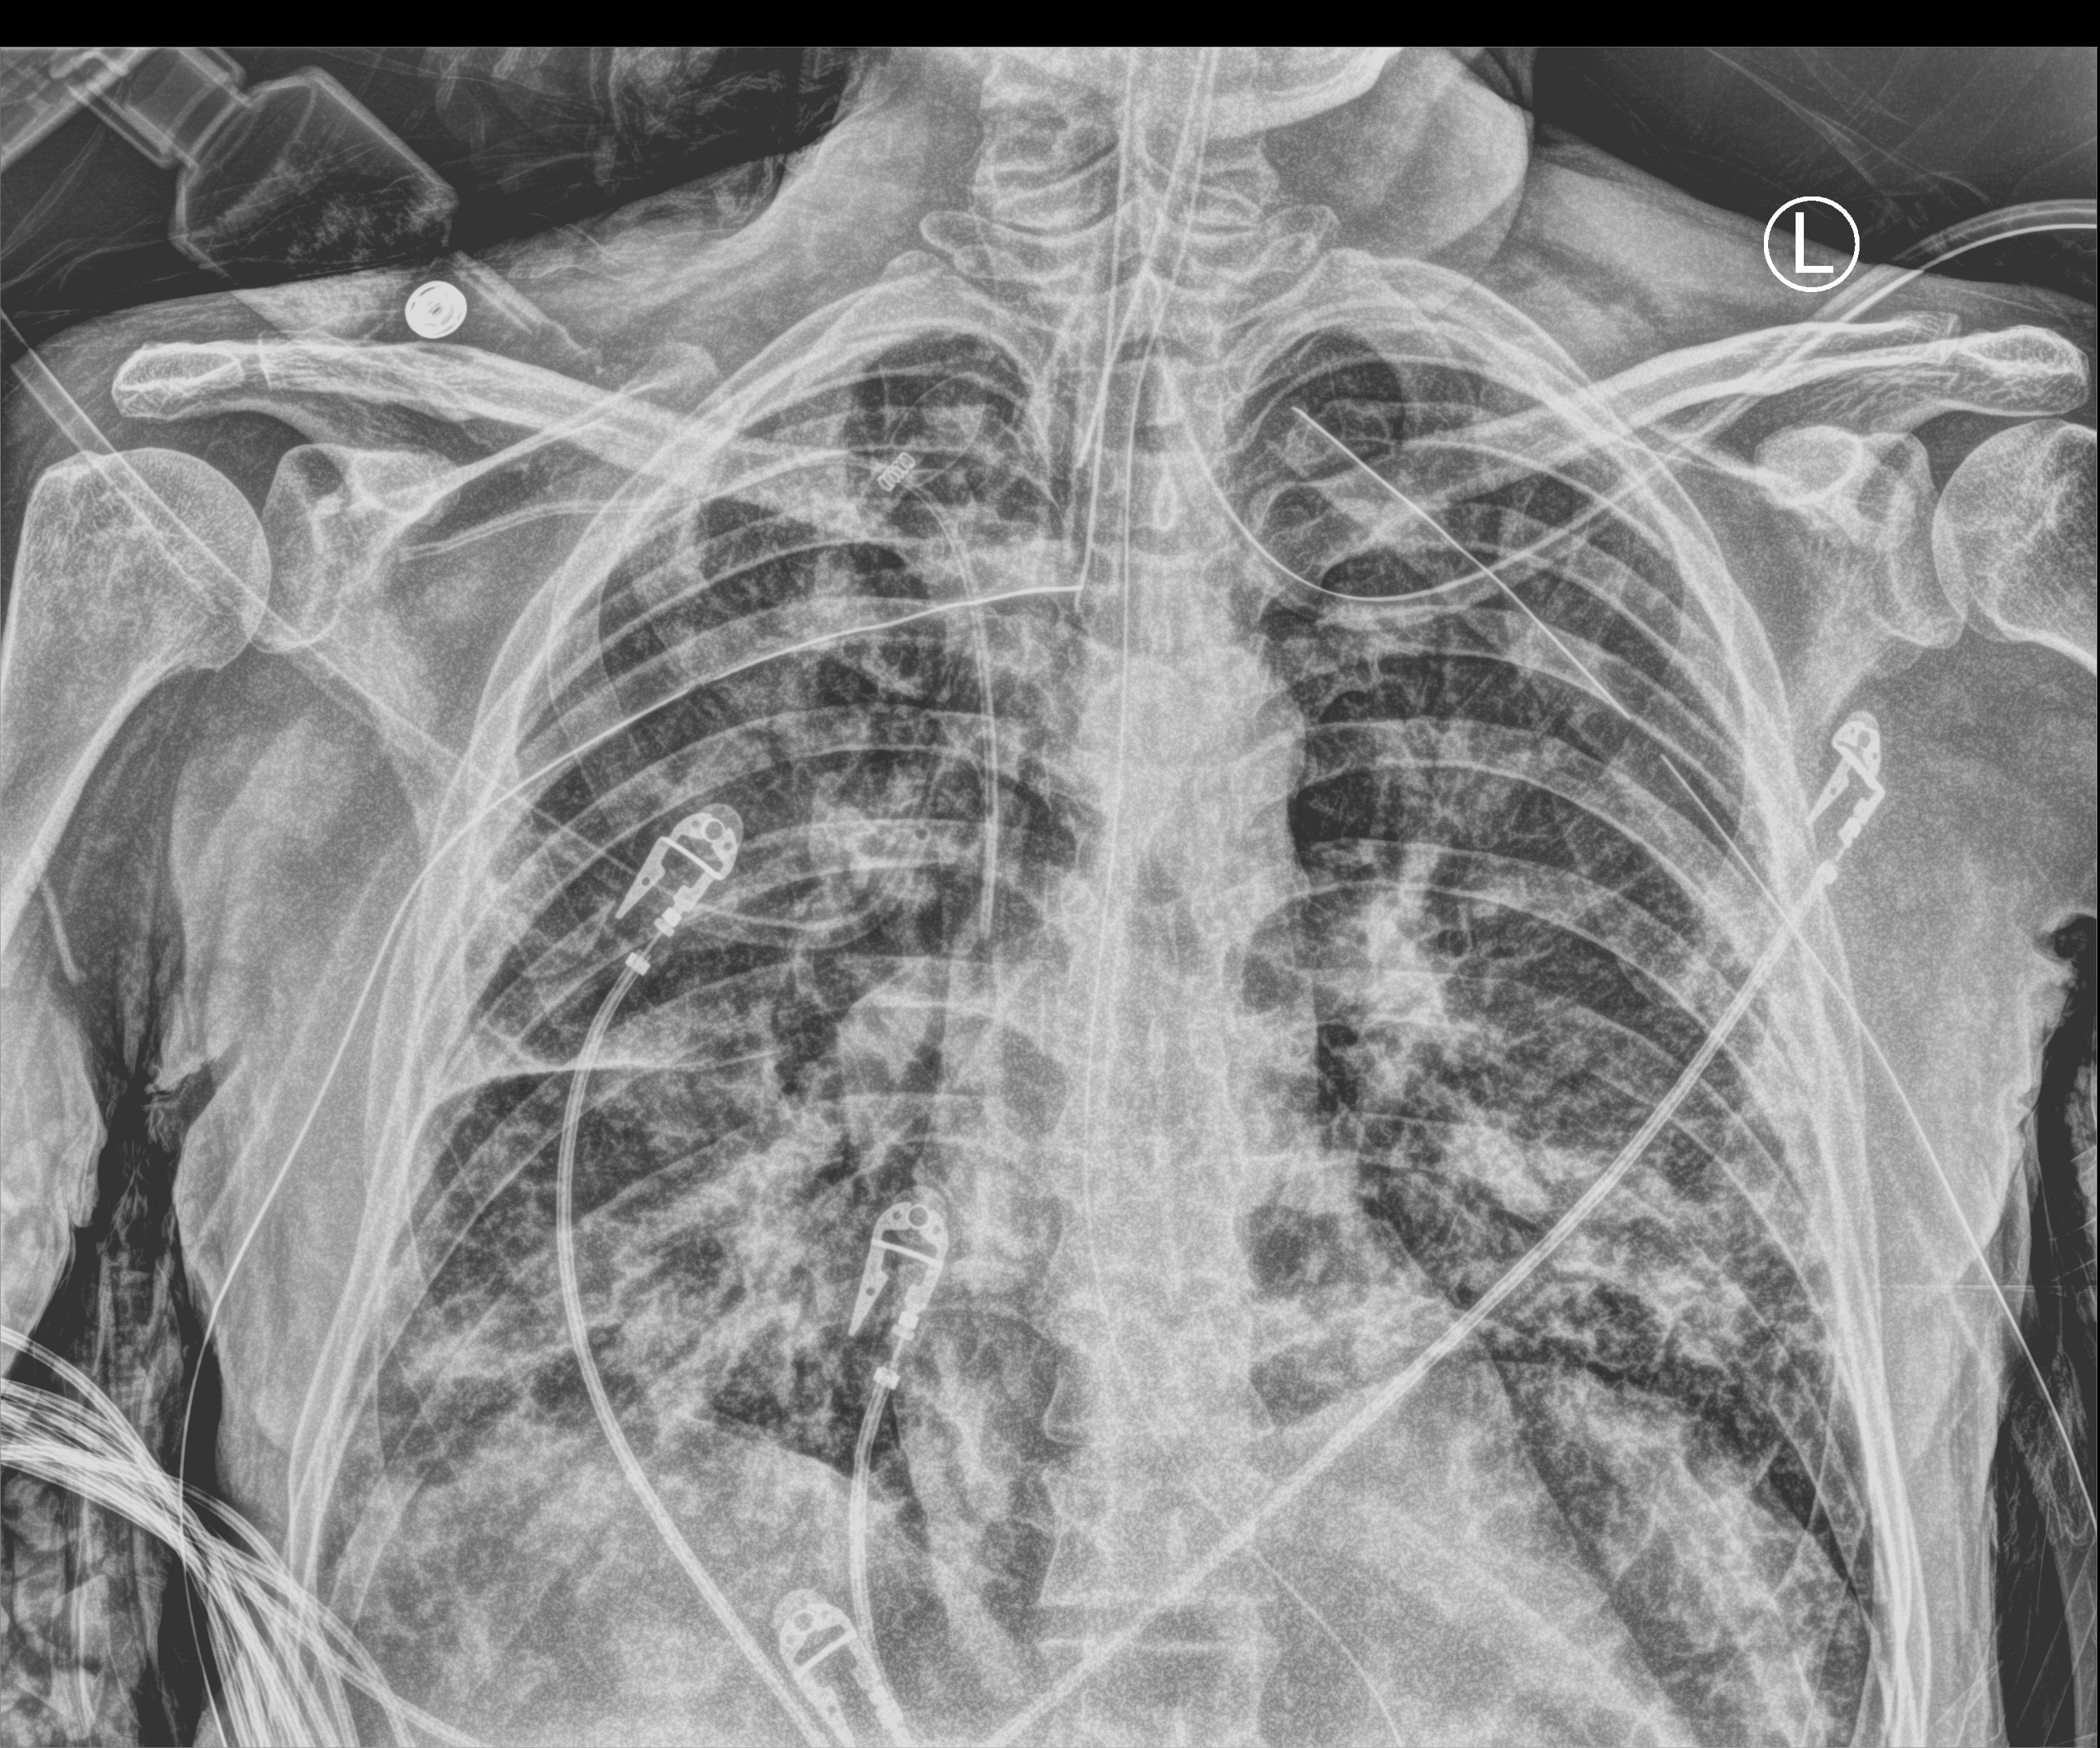
Chest X-ray (portable). Male patient hospitalised with COVID-19, age 18–59 years.
From the hospital-stay record, not from the radiograph (when in the stay this image was taken is not recorded):
- hypertension (admission record): yes
- length of hospital stay: 96 days